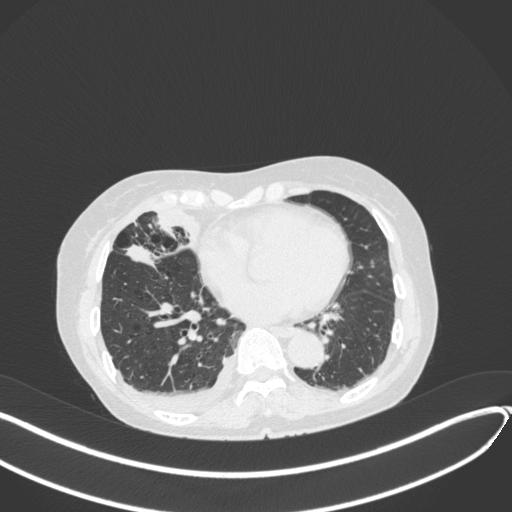
Chest CT, one axial slice. Slice 151 of 418 in the series (ordered by position). Lung window (W 1500 / L -600 HU). 1 mm slice thickness. 512 × 512 image matrix. Female patient, age 75 years. From the clinical record (not read from this slice): clinical TNM (as recorded): T2a N3 M0.
Structures marked on this image (bounding box drawn by a radiologist):
- lung tumour (recorded histology: adenocarcinoma): bounding box (x1, y1, x2, y2) in pixels: (123, 237, 162, 272)